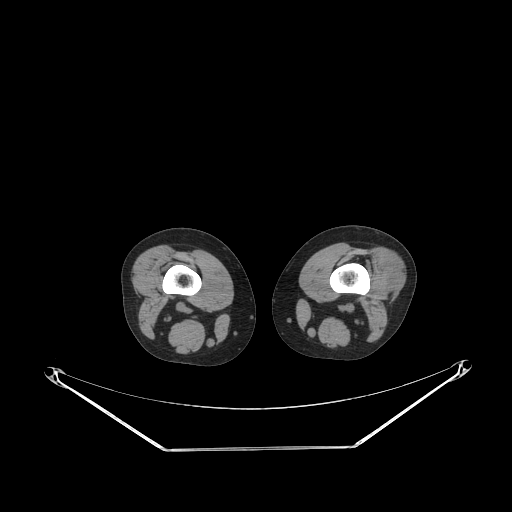
CT of an extremity soft-tissue mass (from a PET/CT study), one axial slice; position 178 of 223 along the scan axis; 140 kVp; soft-tissue window (W 400 / L 40 HU); 3.75 mm slice thickness; 512 × 512 image matrix. Female patient. From the clinical record (not read from this slice): histological type: spindle cell suggestive of biphasic synovial sarcoma; grade: intermediate; site of the primary tumour: left knee.
Structures marked on this image (expert contour drawn on MRI and transferred to this co-registered scan by the dataset authors):
- gross tumour volume including surrounding oedema: bounding box <379,247,405,293> (left, top, right, bottom; pixels)
- gross tumour volume (mass): <379,247,405,293>